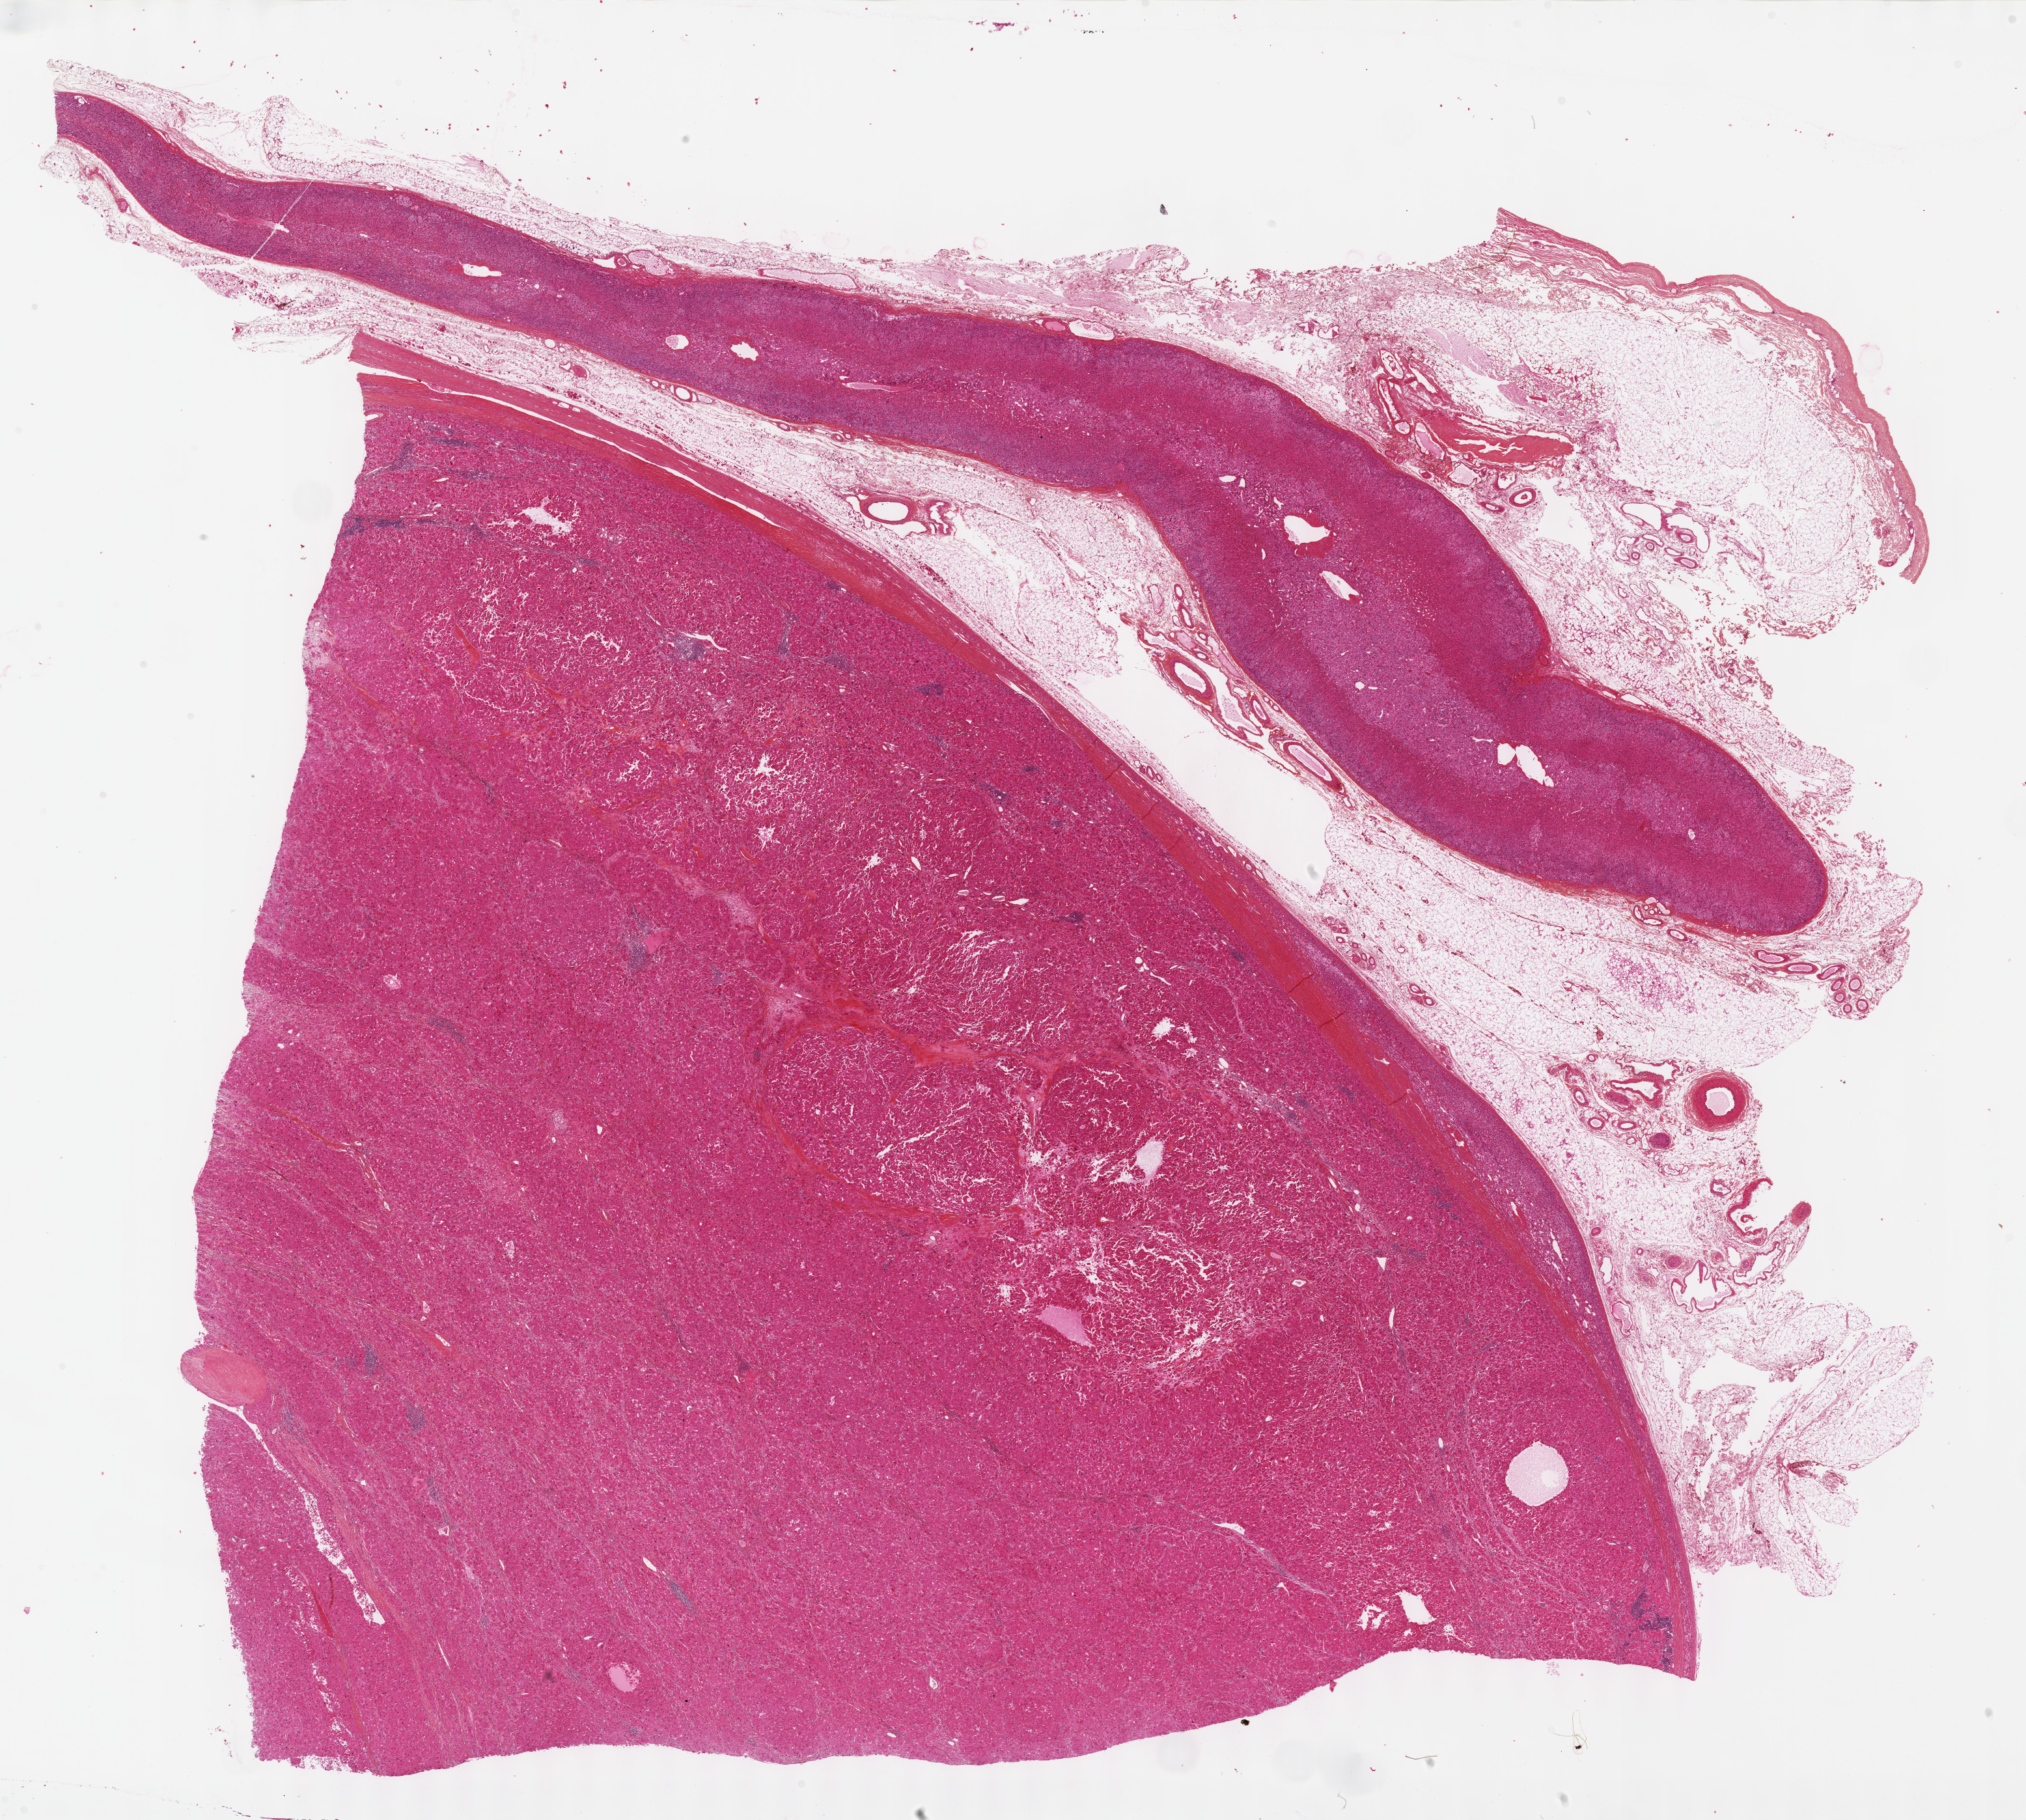
Whole-slide histology image, Hematoxylin and eosin (H&E) stained, whole scanned area (about 25.1 x 22.6 mm) shown as a low-resolution overview; formalin-fixed paraffin-embedded (FFPE) diagnostic section; sample: primary tumour, adrenal cortex. Patient: female, age at initial diagnosis 37 years.
Pathologic diagnosis: Adrenal cortical carcinoma (cortex of adrenal gland). Lymph nodes positive (case pathology): 0 of 21 examined.